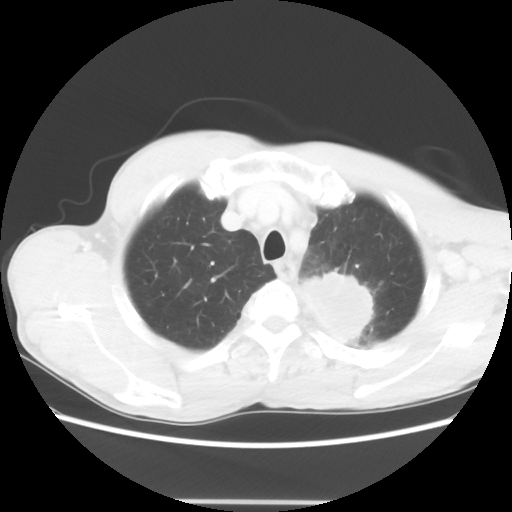
Chest CT, one axial slice. Position 54 of 62 along the scan axis. Reconstruction kernel STANDARD. 100 kVp. Lung window (W 1500 / L -600 HU). 512 × 512 image matrix, field of view 360 × 360 mm. Male patient, age 61 years. From the clinical record (not read from this slice): clinical TNM (as recorded): T3 N1 M1.
Outlined on this slice (bounding box drawn by a radiologist):
- lung tumour (recorded histology: adenocarcinoma): bounding box [x1, y1, x2, y2] px = [296, 269, 397, 352]